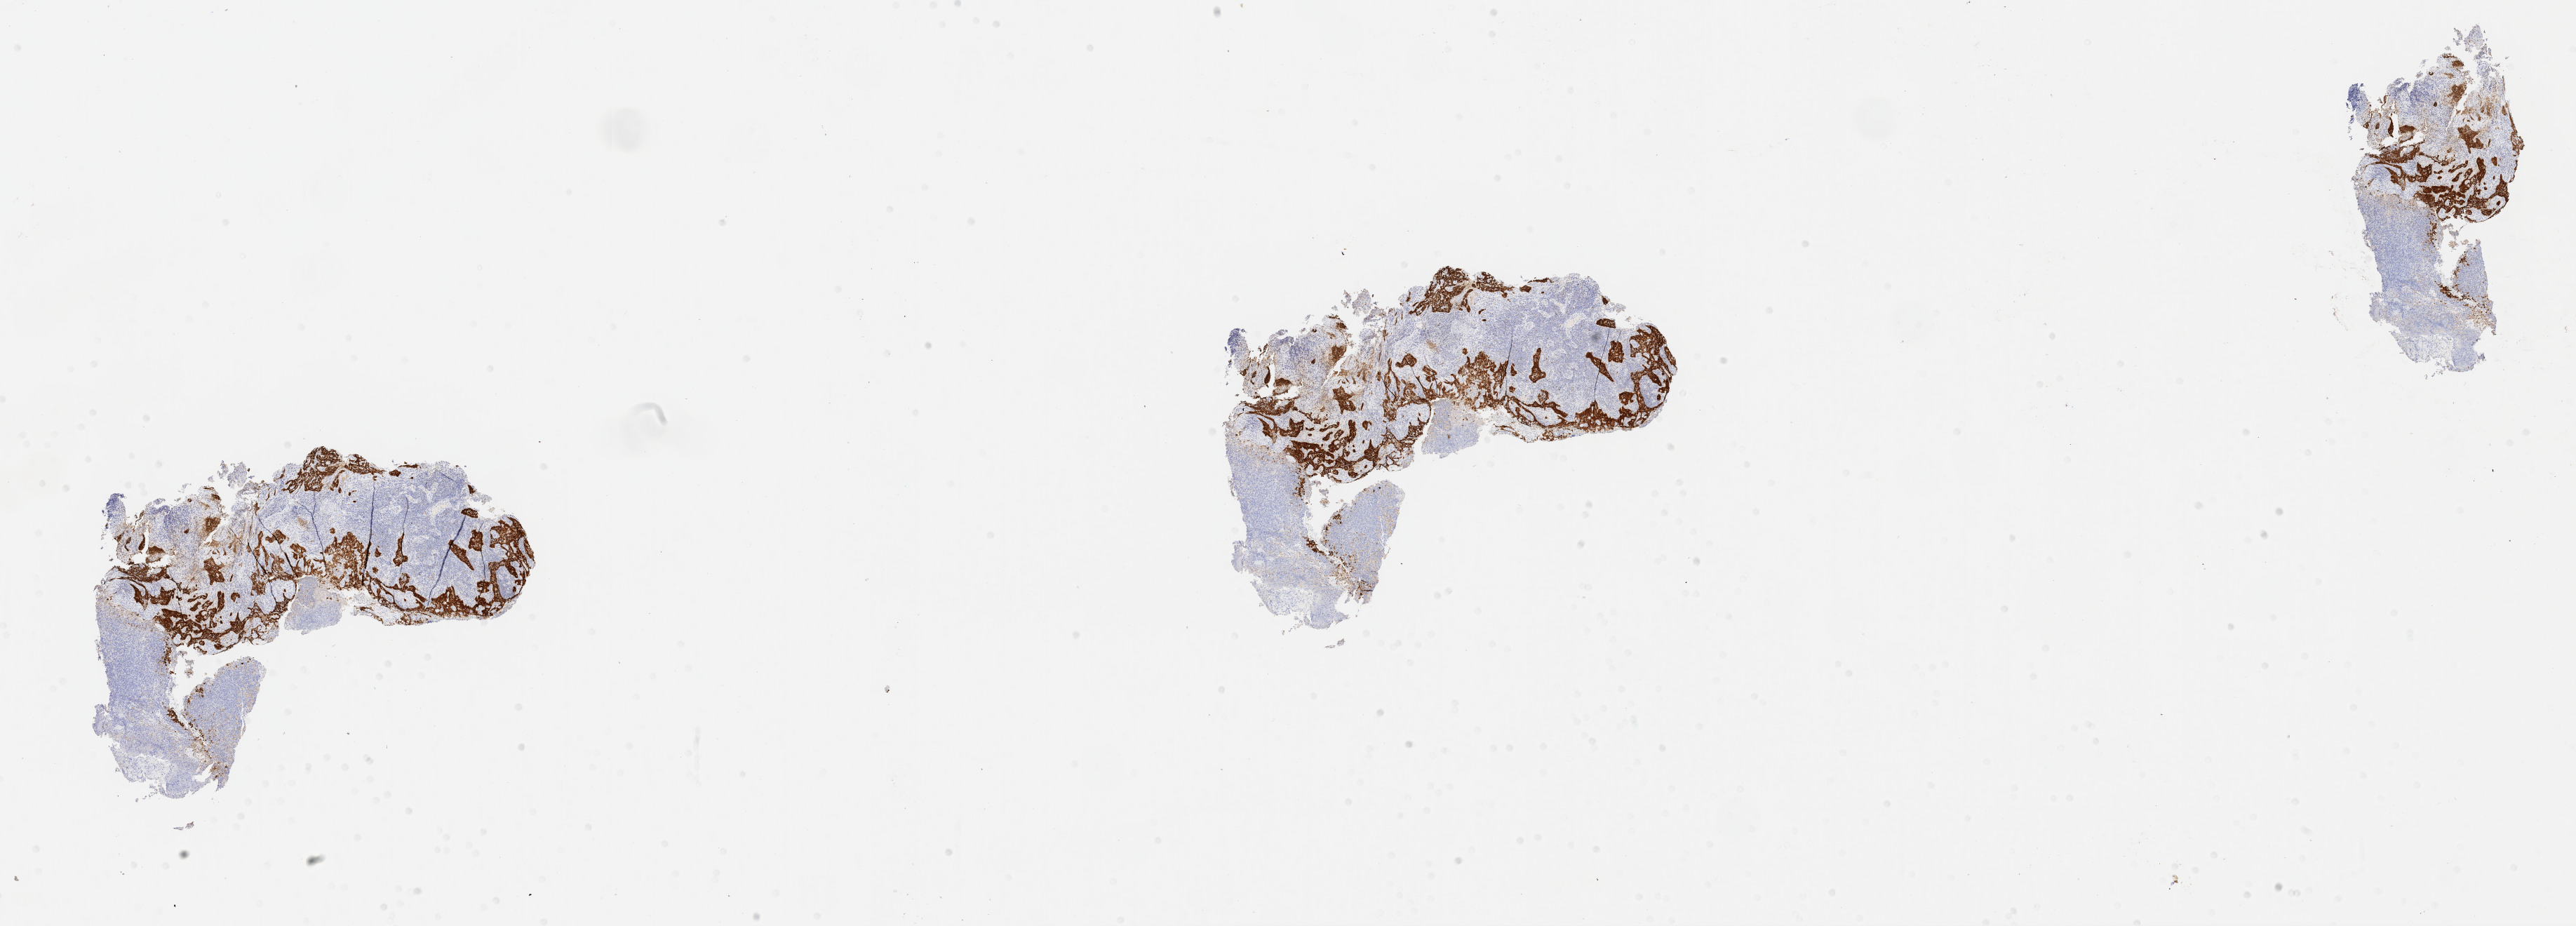
Whole-slide image, immunohistochemical stain for p16 (p16INK4a) — low-resolution overview of the scanned area, about 29.7 x 10.7 mm. Tumor tissue. Site: cervix. Patient: female, aged 39.
Diagnosis: Squamous cell carcinoma, large cell, nonkeratinizing, NOS.